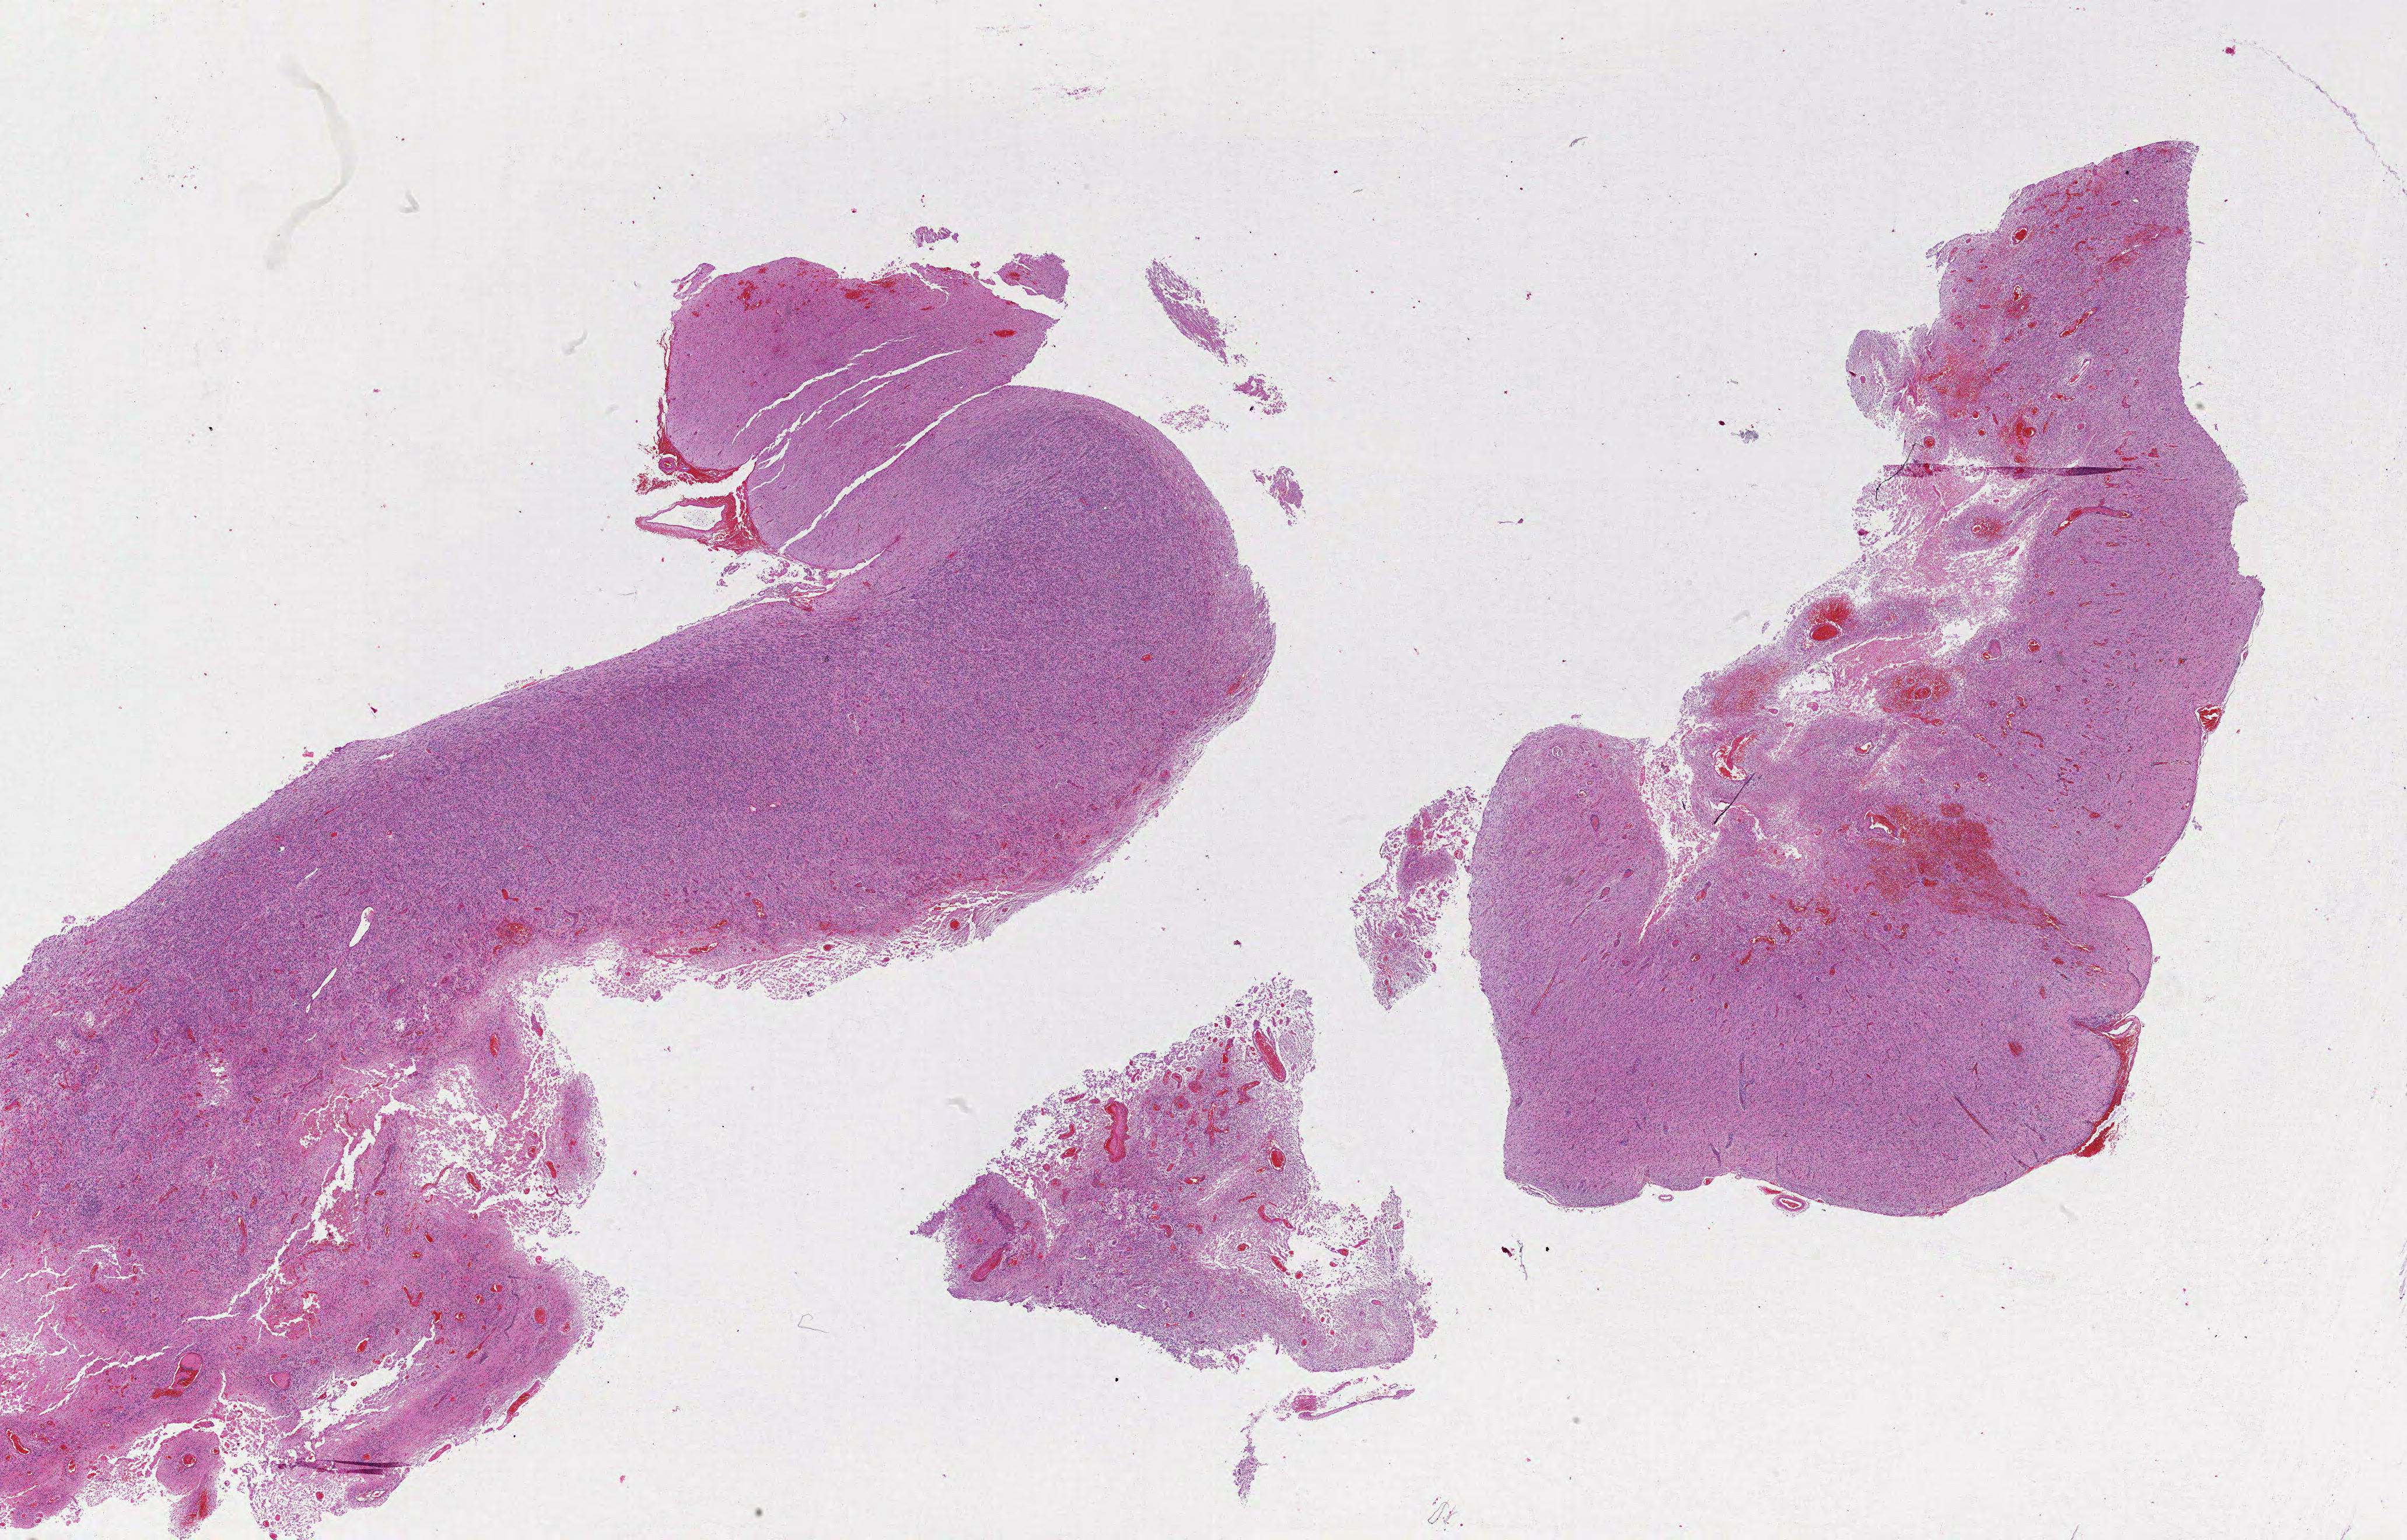
H&E-stained whole-slide image — a low-resolution overview of the entire scanned area, about 33.0 x 21.1 mm; FFPE section; brain, primary tumour sample. Patient: male, age at initial diagnosis 55 years.
Pathologic diagnosis: Glioblastoma.